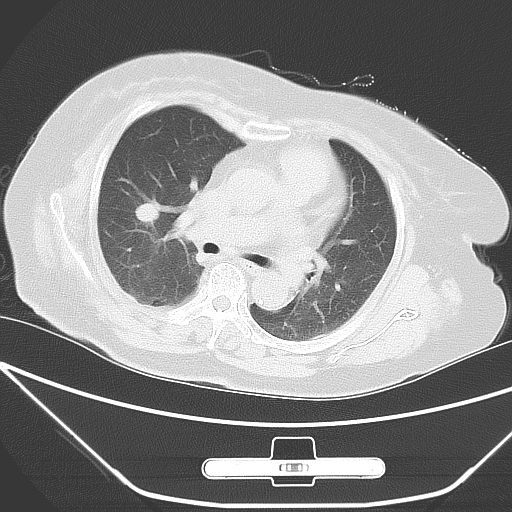
Chest CT, one axial slice; 120 kVp; lung window (W 1500 / L -600 HU); 5 mm slice thickness; 512 × 512 image matrix, field of view 365 × 365 mm. Patient: female, 65 years. From the clinical record (not read from this slice): clinical TNM (as recorded): T1c N0 M0.
Annotated regions visible in this slice (rectangle marked by the reading radiologist):
- lung tumour (recorded histology: adenocarcinoma): box from (x=131, y=195) to (x=165, y=235) px